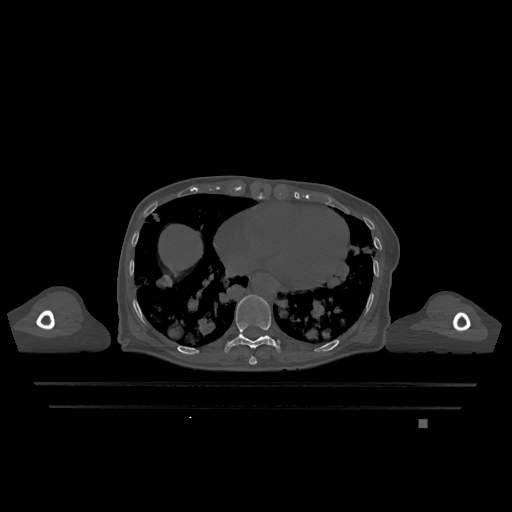
CT including the spine, one axial slice. Slice 643 of 1317 in the series (ordered by position). Bone window (W 1800 / L 400 HU). 512 × 512 image matrix. Female patient, age 74 years. Case-level facts recorded for this patient, not image findings: primary cancer: lung.
Annotated regions visible in this slice (semi-automatic segmentation, software-assisted and operator-edited):
- T10 vertebra: bounding box <224,295,281,353> (left, top, right, bottom; pixels)
- T9 vertebra: <249,356,257,365>